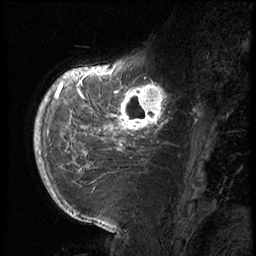
Breast MRI (dynamic contrast-enhanced), one sagittal slice; slice 21 of 72 in the series (ordered by position); 3 images stored at this slice position (order not interpretable as contrast timing); 1.5 T; TE 4.2 ms, TR 8.9 ms; 2.5 mm slice thickness; 256 × 256 image matrix, field of view 200 × 200 mm. Patient: female, 56 years. Case-level facts recorded for this patient, not image findings: setting: breast cancer imaged before/during neoadjuvant chemotherapy.
Structures marked on this image (semi-automatically segmented with operator editing):
- analysis volume of interest (the breast-tissue region the enhancement analysis was run in; not a lesion): bounding box <114,76,177,138> (left, top, right, bottom; pixels)
- tumour enhancement mask (voxels above the 140 % enhancement threshold inside the analysis volume of interest): <115,82,167,131>